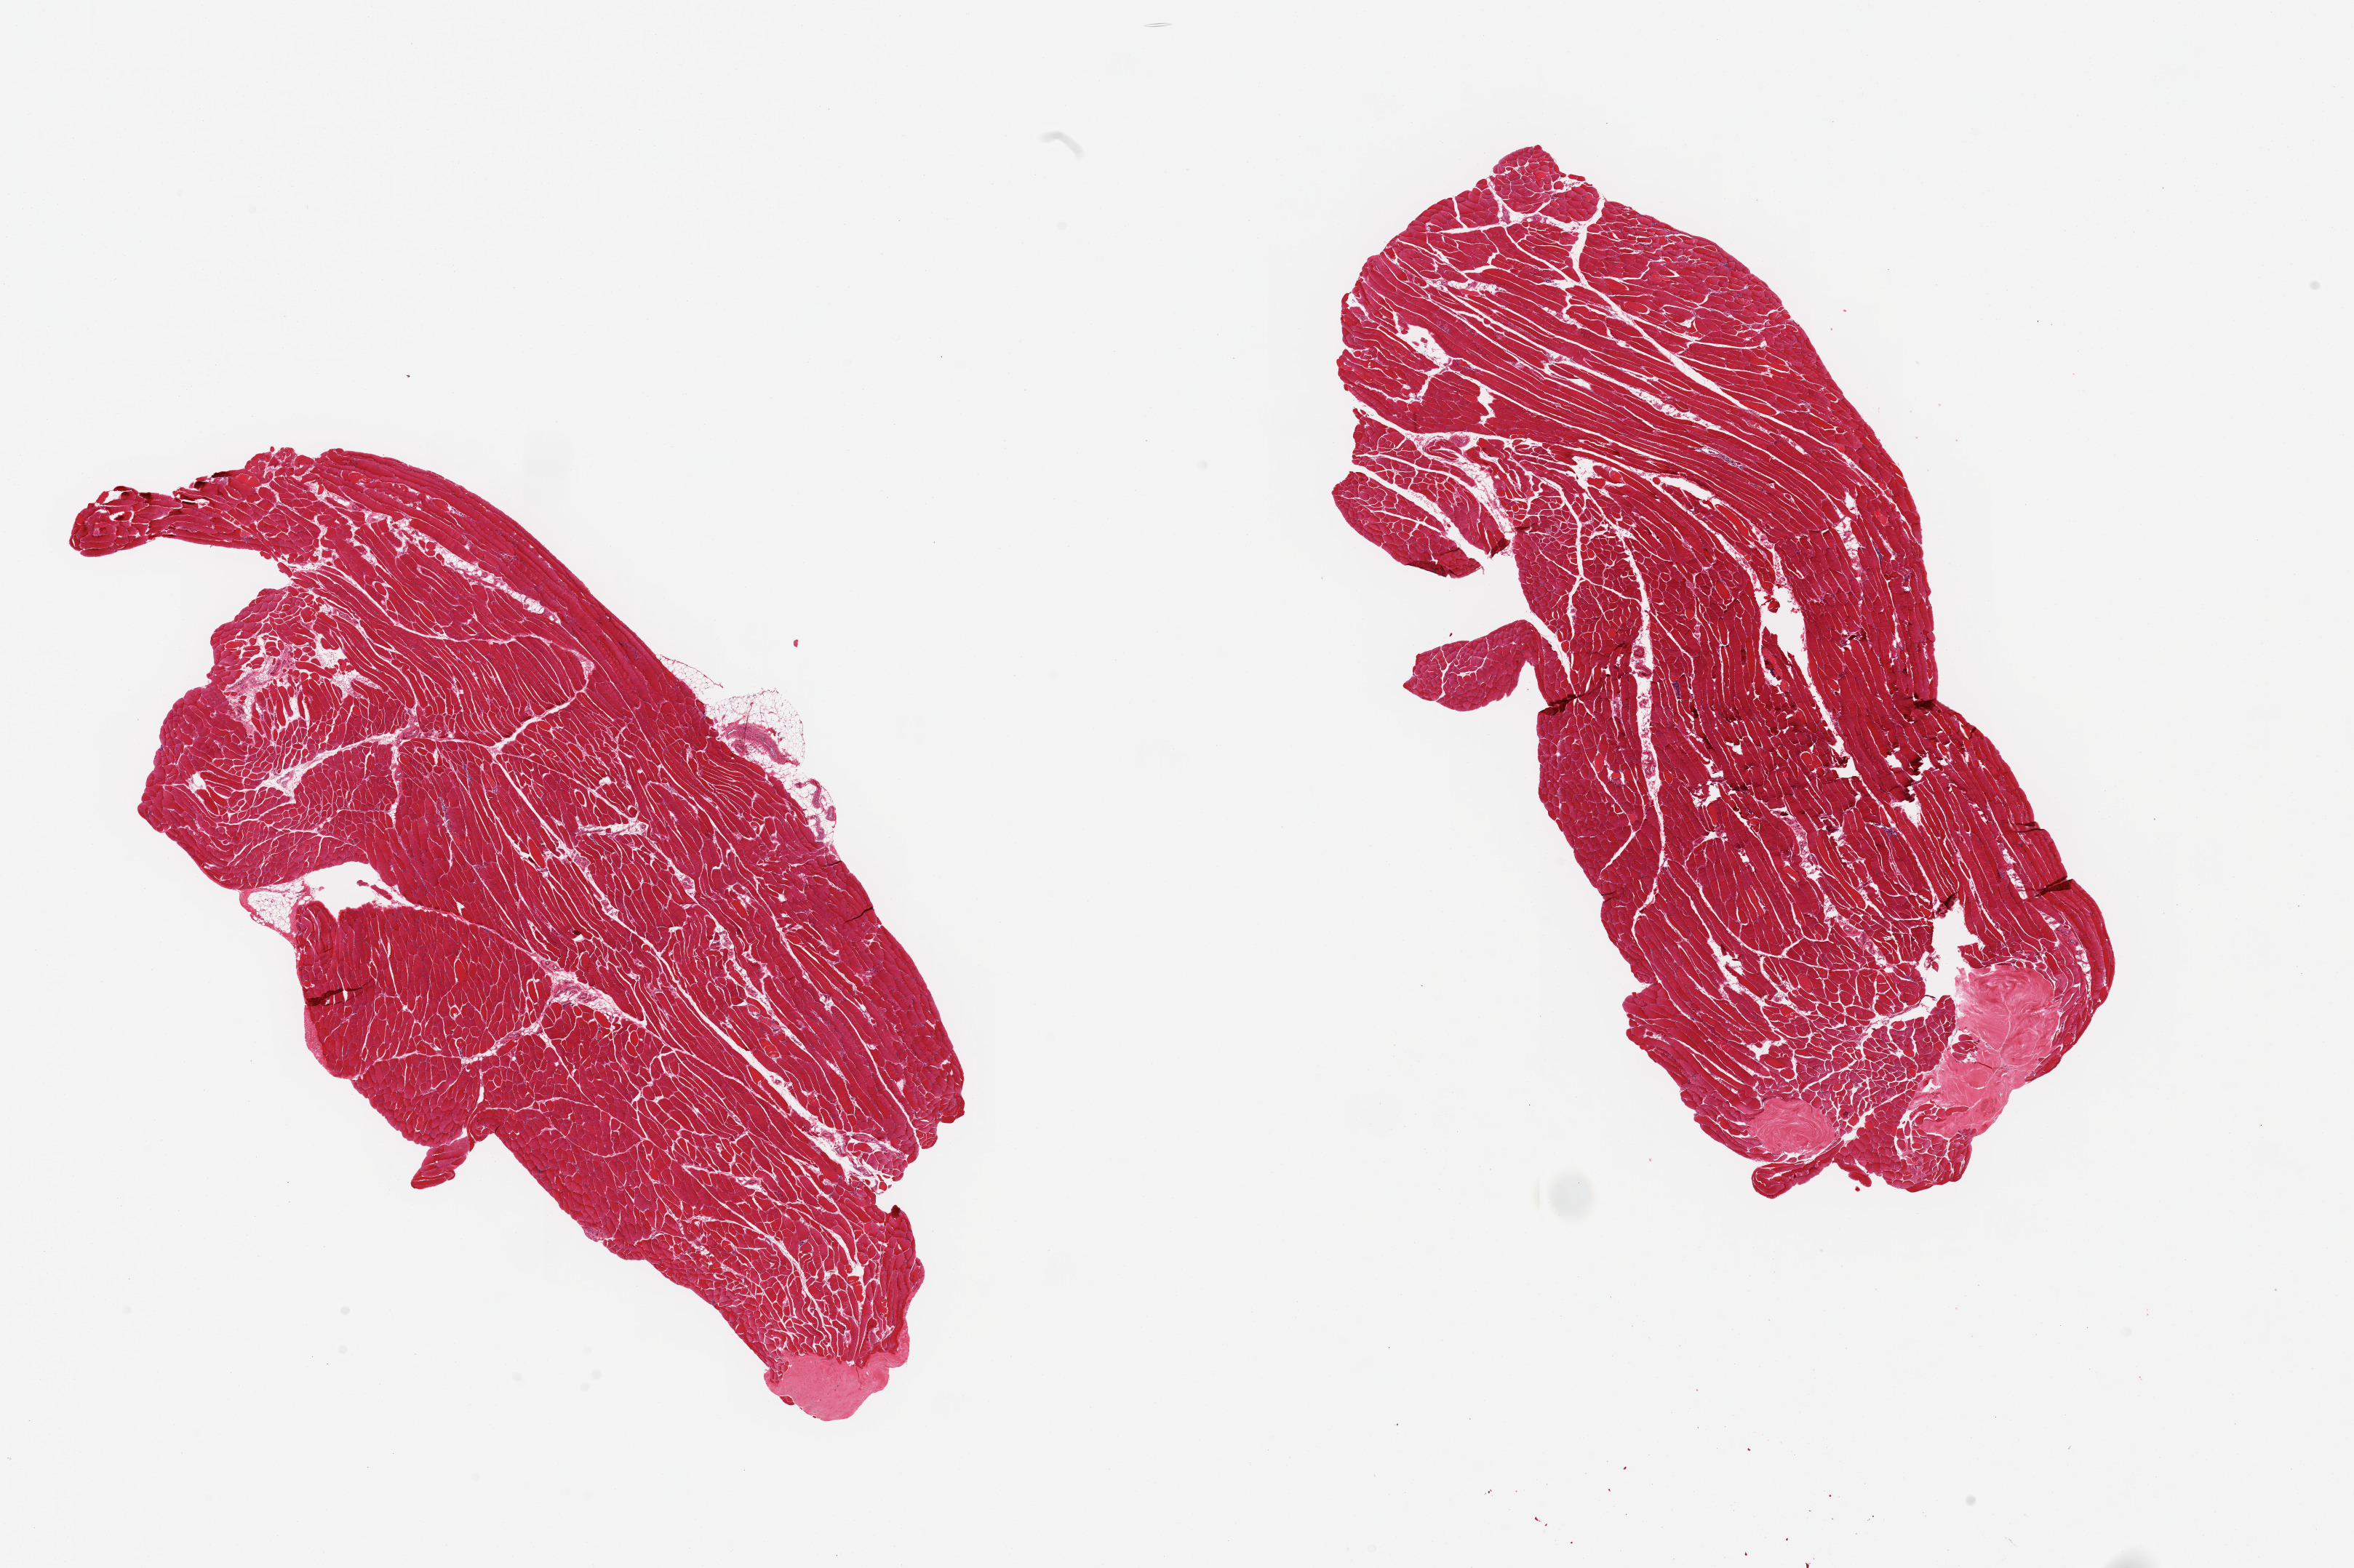
Whole-slide image, H&E stain, brightfield, whole scanned area (about 25.6 x 17.1 mm) shown as a low-resolution overview. PAXgene-fixed, paraffin-embedded tissue. Target tissue: skeletal muscle. Donor tissue sample. Donor: male.
Pathologist's review note for this sample: 2 pieces, ~5-10% interstitial fat or tendon insertion site.